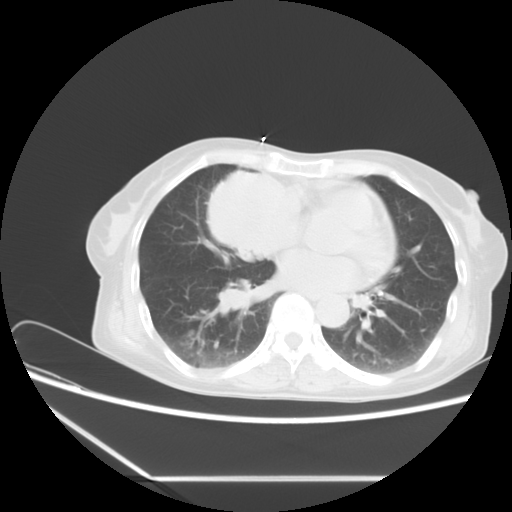
Chest CT, one axial slice. Slice 2 of 16 in the series (ordered by position). Reconstruction kernel STANDARD. 120 kVp. Lung window (W 1500 / L -600 HU). 512 × 512 image matrix, field of view 350 × 350 mm. Patient: female, 63 years. Case-level facts recorded for this patient, not image findings: clinical TNM (as recorded): T2b N1 M0.
Annotated regions visible in this slice (rectangle marked by the reading radiologist):
- lung tumour (recorded histology: adenocarcinoma): bounding box (x1, y1, x2, y2) in pixels: (201, 156, 303, 269)